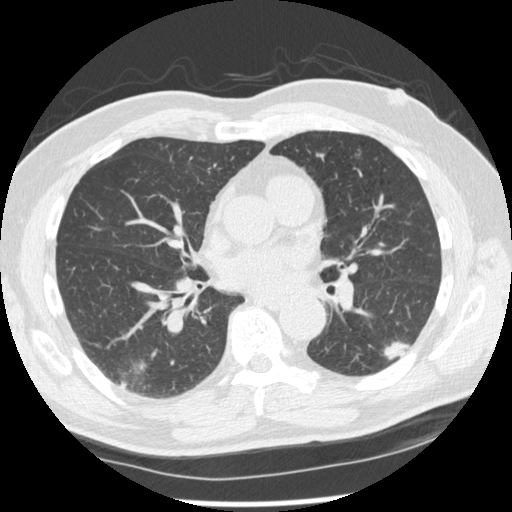
Axial slice from a low-dose chest CT screening exam, second screening round (one year after baseline), lung window (W 1500 / L -600 HU), standard (soft-tissue) reconstruction kernel (STANDARD). Male participant, aged 74 years at enrolment. Former smoker at enrolment.
- Expert-annotated lung lesion, bounding box <366,312,425,368> (left, top, right, bottom; pixels).
- The screening reader recorded 7 non-calcified nodules or masses ≥4 mm on this exam (right upper lobe, right lower lobe, right upper lobe, right lower lobe, left lower lobe, left upper lobe, left upper lobe); which of them this box marks is not recorded.
- Official screen result: positive, other.
- Later outcome: lung cancer diagnosed 43 days after this screen — squamous cell carcinoma, NOS, left lower lobe, well differentiated (G1), stage IA (AJCC 6th edition), 28 mm at pathology.